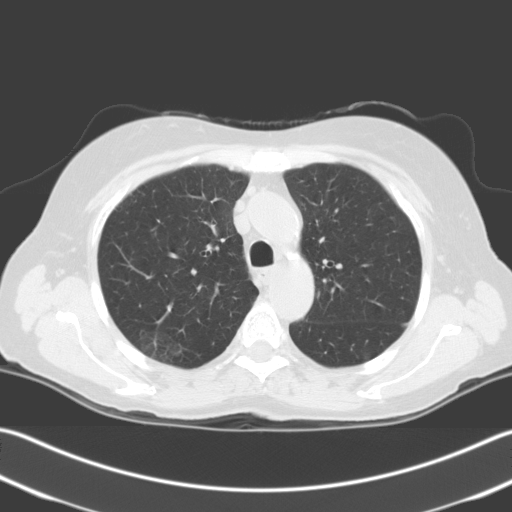
Axial slice from a low-dose chest CT screening exam; first (baseline) screen; lung window (W 1500 / L -600 HU); standard (soft-tissue) reconstruction kernel (C); 140 kVp; slice 49 of 204 in the series. Female participant, aged 67 years at enrolment. Current smoker at enrolment.
Expert-annotated lung lesion, box from (x=126, y=324) to (x=189, y=373) px. The screening reader recorded 2 non-calcified nodules or masses ≥4 mm on this exam (right upper lobe, right upper lobe); which of them this box marks is not recorded. Official screen result: positive, change unspecified: nodule(s) >= 4 mm or enlarging nodule(s), mass(es), or other non-specific abnormalities suspicious for lung cancer.